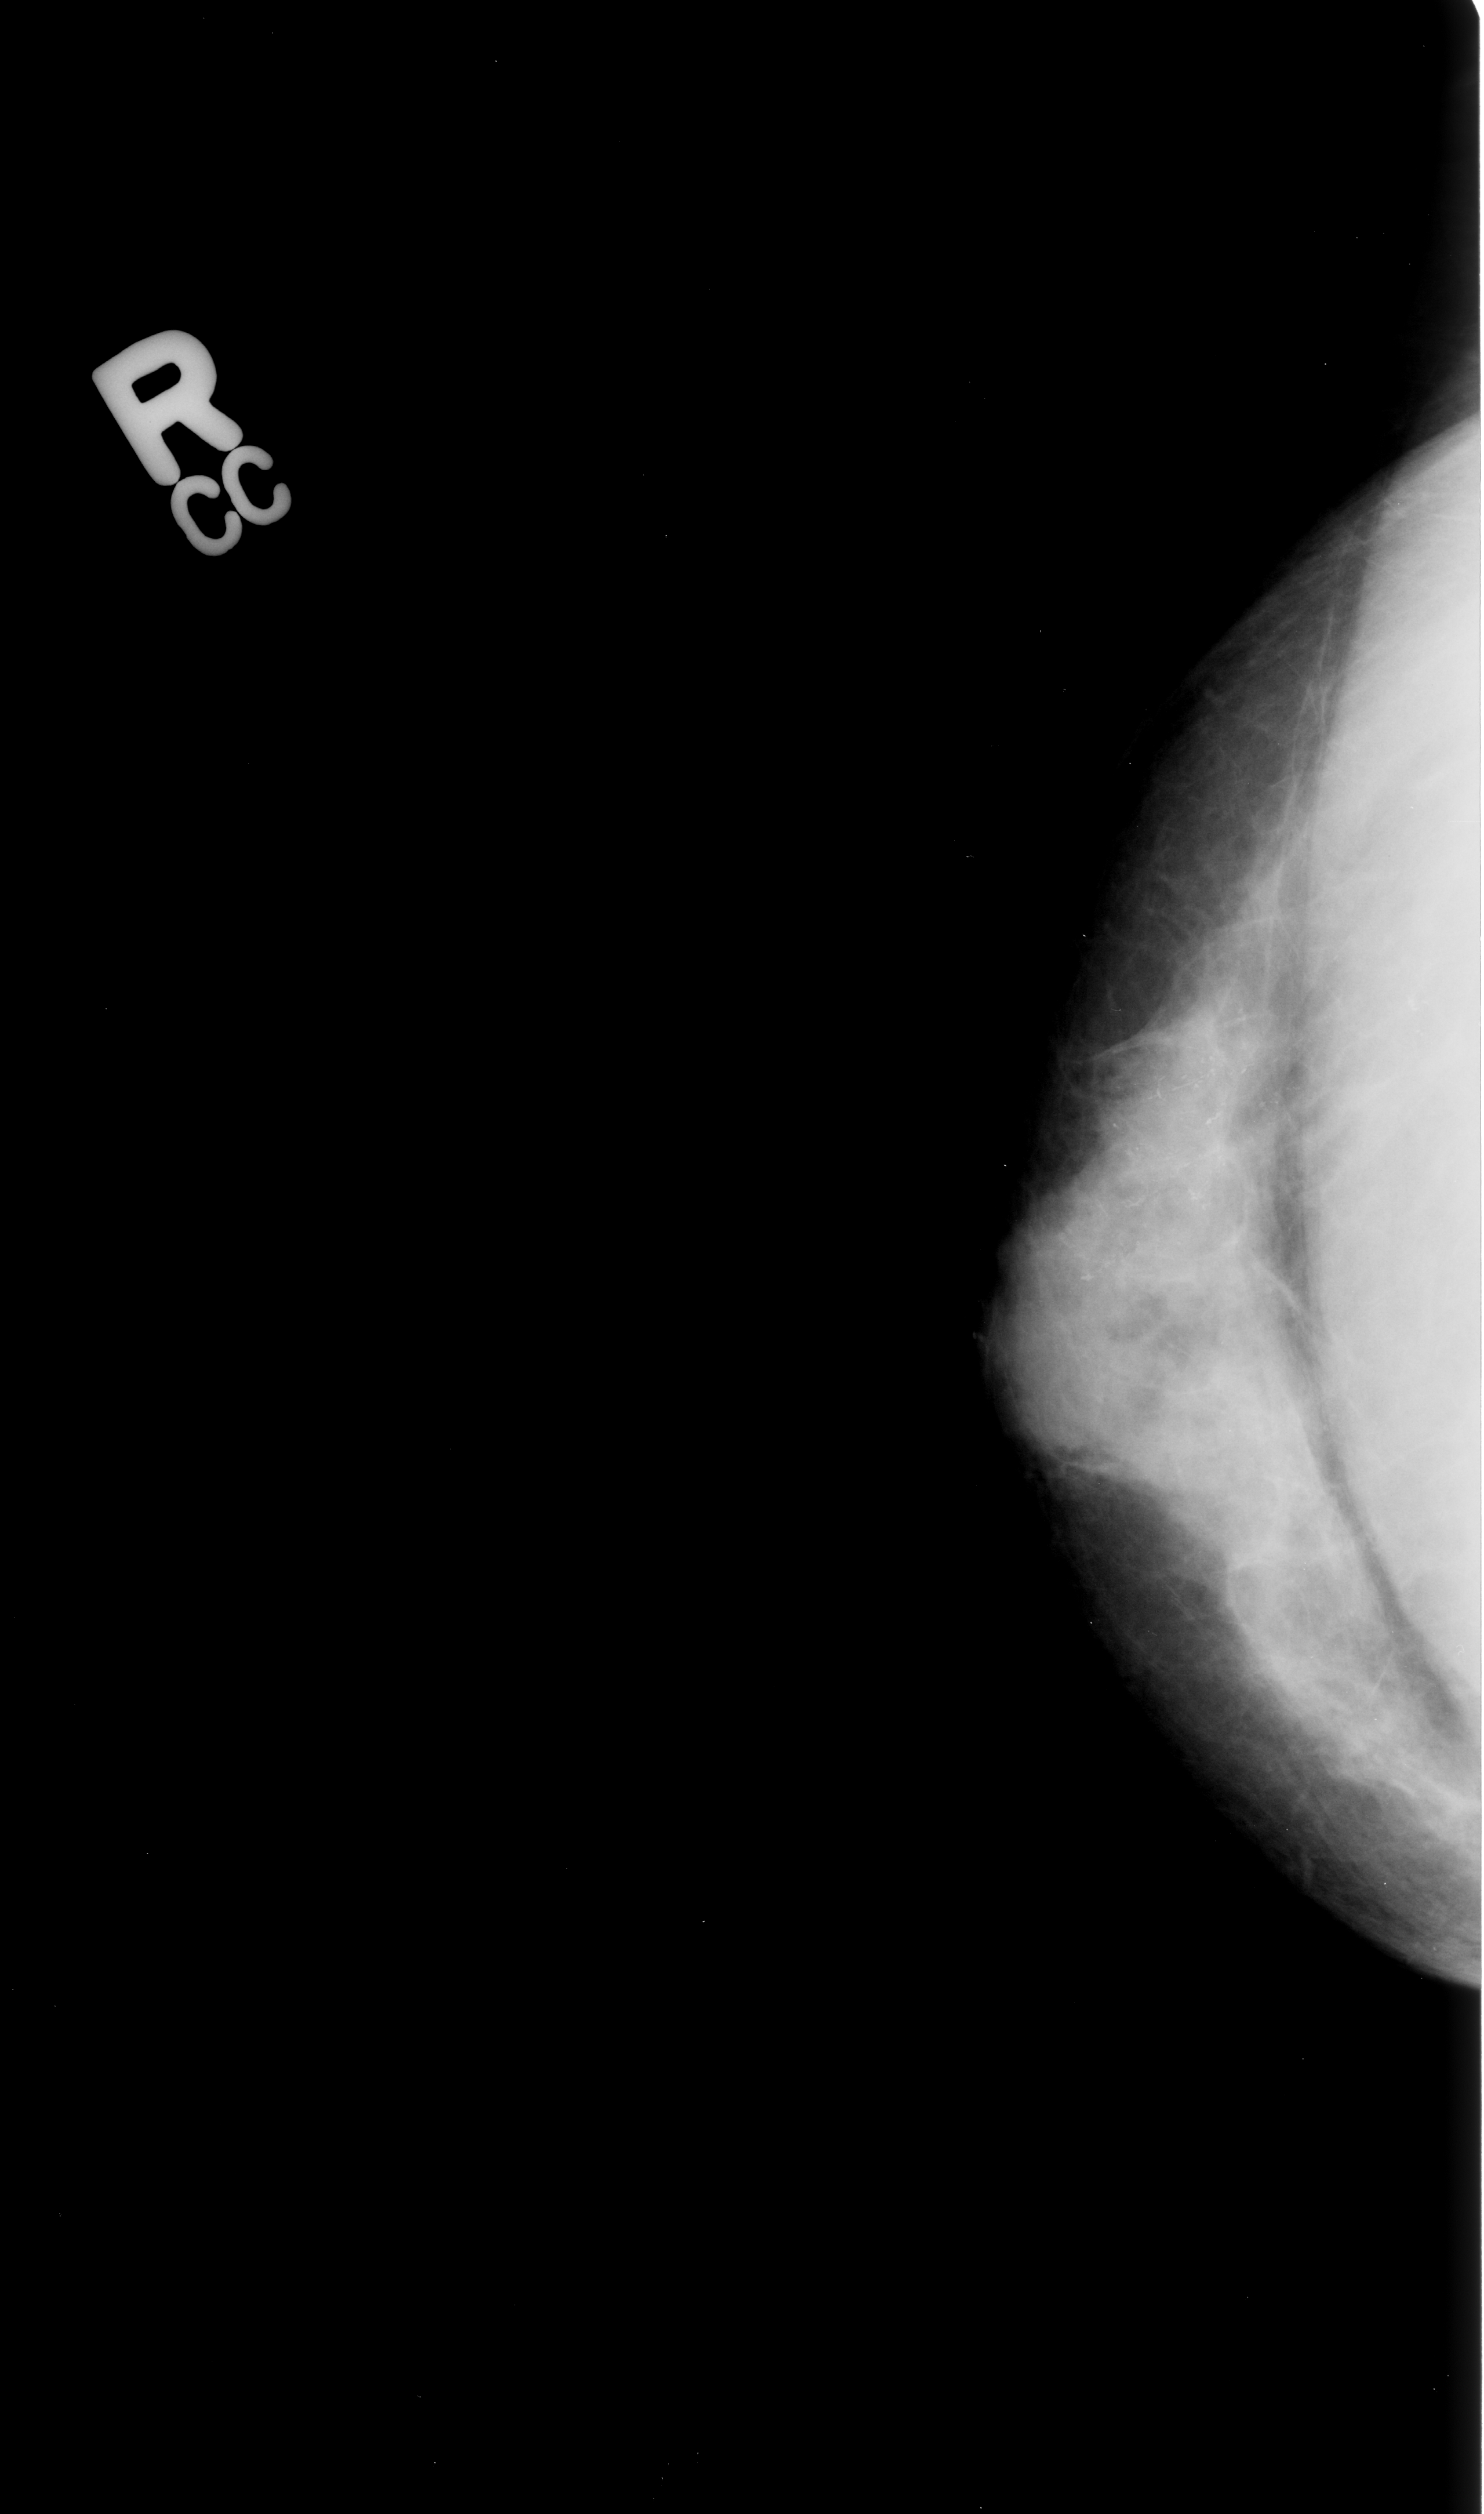
Mammogram (digitized film); right breast; craniocaudal (CC) view; BI-RADS breast density category 3 (scale 1–4); 1484 × 2514 image matrix.
Expert-marked regions of interest on this film, with their recorded descriptors:
- calcifications, morphology fine linear branching, distribution linear / segmental; BI-RADS assessment category 5; pathology (as recorded): malignant: bounding box [x1, y1, x2, y2] px = [1015, 1001, 1453, 1355]